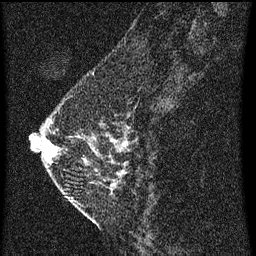
Breast MRI (dynamic contrast-enhanced), one sagittal slice. Position 21 of 60 along the scan axis. Dynamic contrast-enhanced series, image 2 of 3 at this slice position (ordered by acquisition). 1.5 T. TE 4.2 ms, TR 8 ms. 2 mm slice thickness. 256 × 256 image matrix. Patient: female, 47 years.
Structures marked on this image (semi-automatic segmentation, software-assisted and operator-edited):
- analysis volume of interest (the breast-tissue region the enhancement analysis was run in; not a lesion): bounding box <42,92,140,199> (left, top, right, bottom; pixels)
- tumour enhancement mask (voxels above the 70 % enhancement threshold inside the analysis volume of interest): <46,140,126,165>